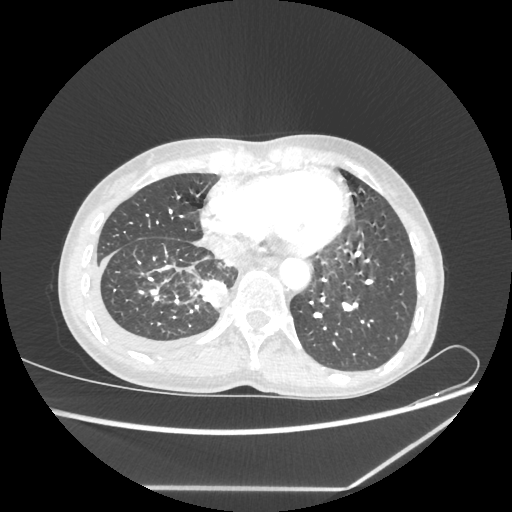
Chest CT, one axial slice; 80 kVp; lung window (W 1500 / L -600 HU); 1.25 mm slice thickness; 512 × 512 image matrix, field of view 364 × 364 mm. Patient: female, 59 years. Case-level facts recorded for this patient, not image findings: clinical TNM (as recorded): T1c N1 M1.
Annotated regions visible in this slice (rectangle marked by the reading radiologist):
- lung tumour (recorded histology: adenocarcinoma): bounding box <197,277,228,310> (left, top, right, bottom; pixels)